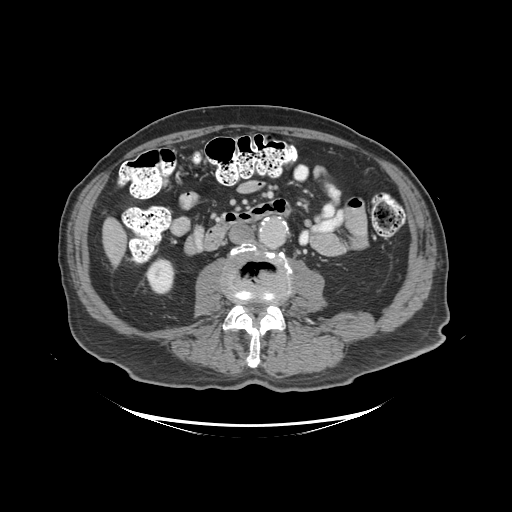
Contrast-enhanced abdominal CT (liver protocol), one axial slice. Position 24 of 99 along the scan axis. Reconstruction kernel STANDARD. 140 kVp. Soft-tissue window (W 400 / L 40 HU). 2.5 mm slice thickness. 512 × 512 image matrix, field of view 460 × 460 mm. From the clinical record (not read from this slice): diagnosis: hepatocellular carcinoma (patient treated with transarterial chemoembolisation; whether this scan precedes or follows treatment is not stated here); TNM stage (as recorded): Stage-I; Child-Pugh class: A.
Annotated regions visible in this slice (semi-automatically segmented with operator editing):
- liver parenchyma outside the tumour (the mass and vessels are separate outlines, so this box may not span the whole liver): bounding box (x1, y1, x2, y2) in pixels: (102, 218, 126, 264)